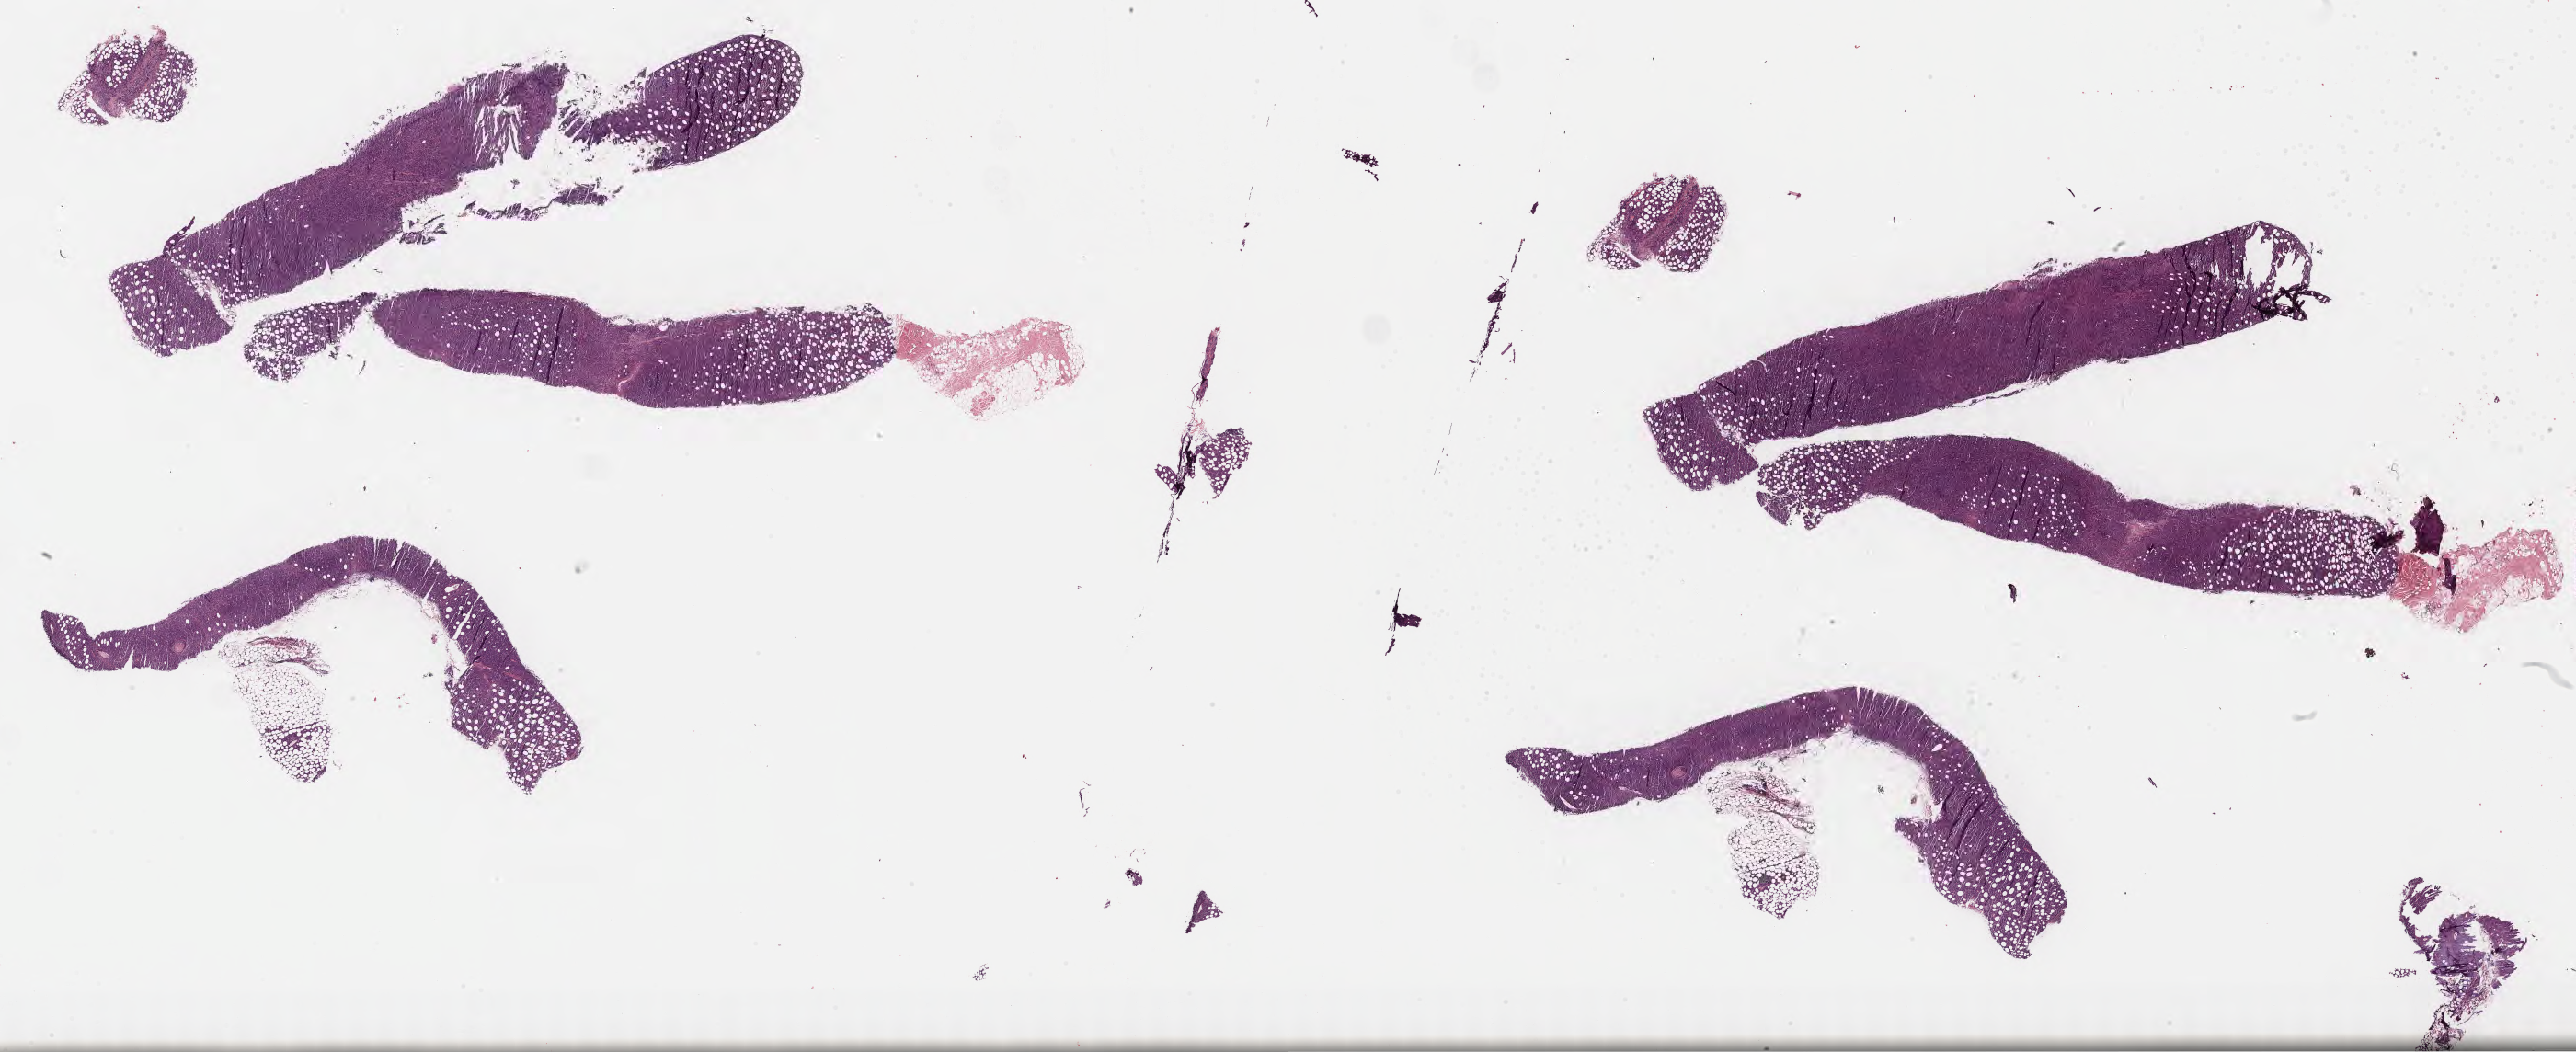
Whole-slide image, hematoxylin and eosin (H&E) stain — a low-resolution overview of the entire scanned area, about 45.3 x 18.5 mm, tumor tissue. Patient: female, age 43 years.
Diagnosis: Burkitt lymphoma, NOS.